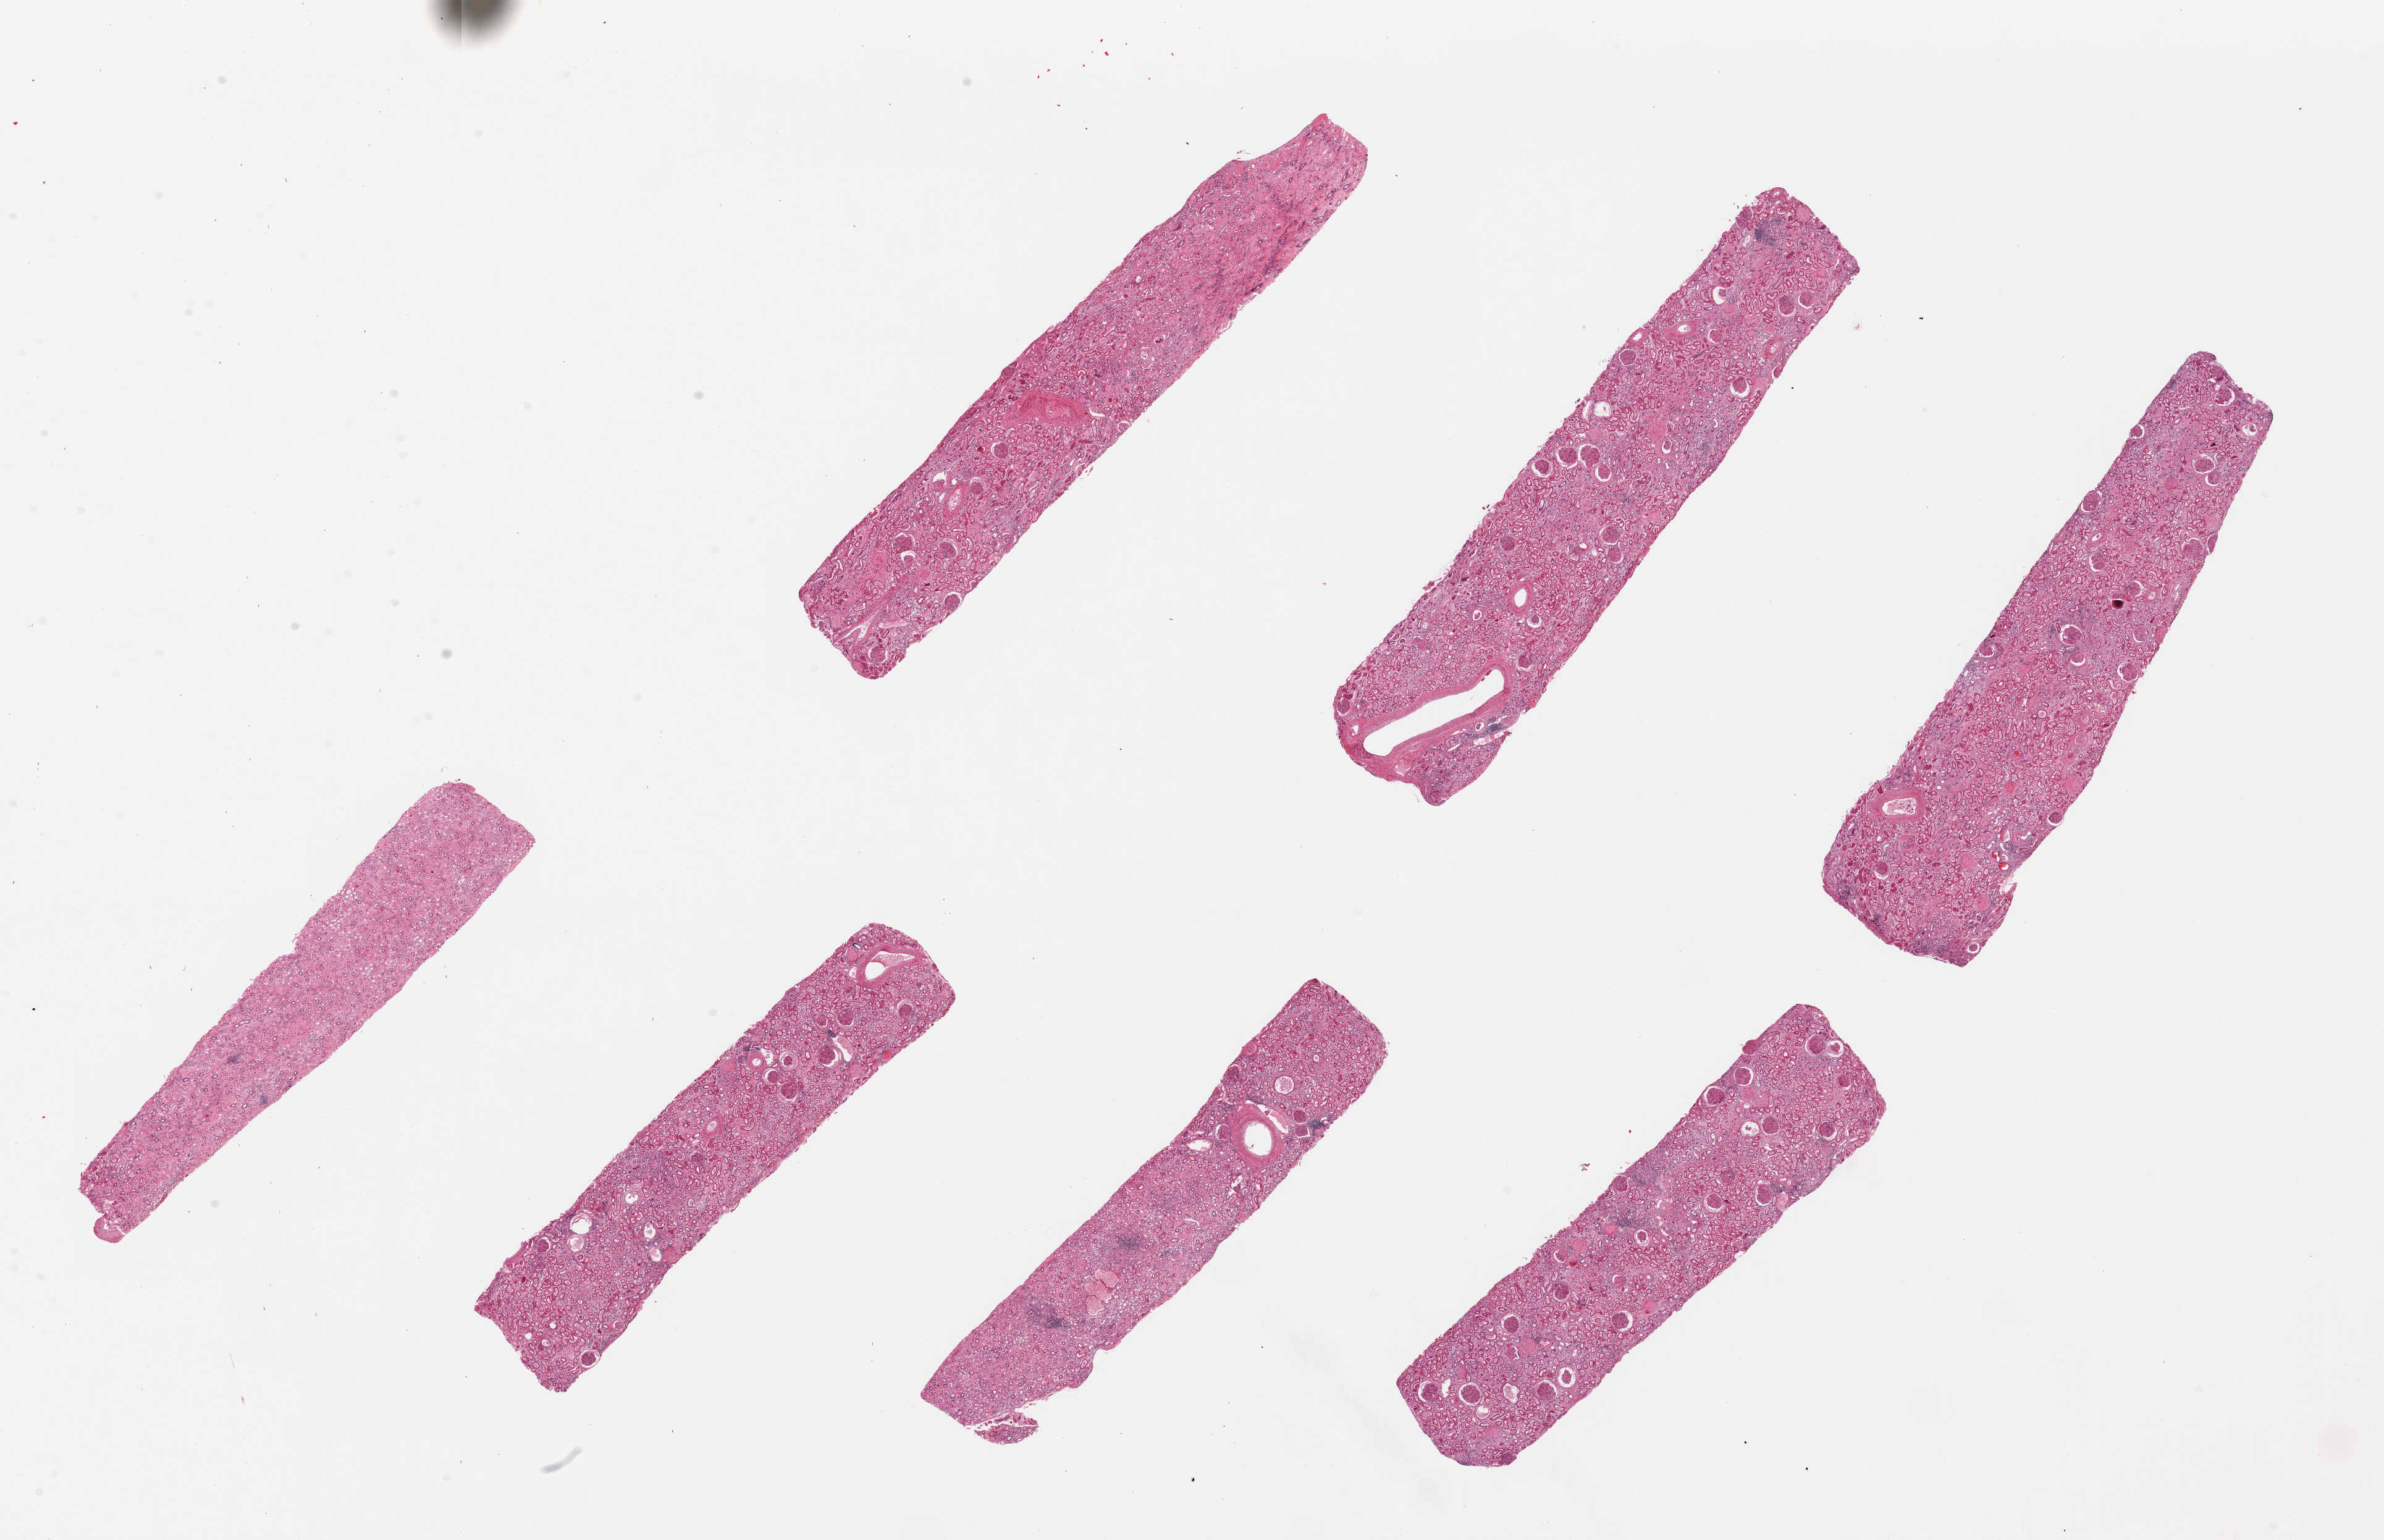
Hematoxylin and eosin (H&E) whole-slide image, shown as a low-resolution overview of the whole scanned area (about 30.5 x 19.7 mm, acquisition: 20x scan); PAXgene-fixed, paraffin-embedded tissue; section of renal cortex (target tissue); donor tissue sample. Donor: female.
Review note (as recorded): 7 pieces, up to 9x2mm; arteriolar and glomerular sclerosis consistent with diabetes; ~80% glomeruli are scarred; one piece and half of another piece are medulla.